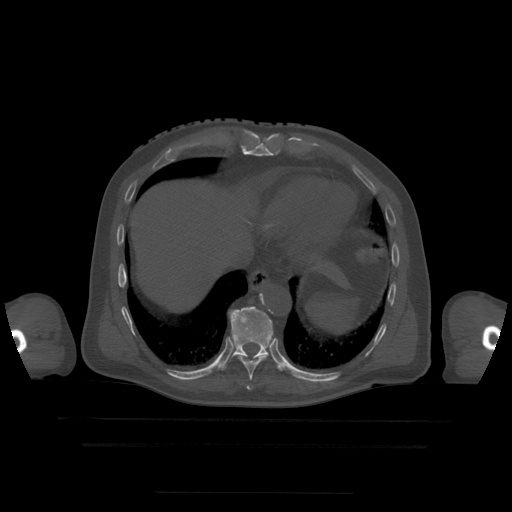
CT including the spine, one axial slice; slice 251 of 522 in the series (ordered by position); bone window (W 1800 / L 400 HU); 512 × 512 image matrix, field of view 436 × 436 mm. Patient age 68 years. Case-level facts recorded for this patient, not image findings: primary cancer: urothelial.
Annotated regions visible in this slice (semi-automatic segmentation, software-assisted and operator-edited):
- T10 vertebra: bounding box <223,307,277,370> (left, top, right, bottom; pixels)
- T9 vertebra: <239,356,268,390>